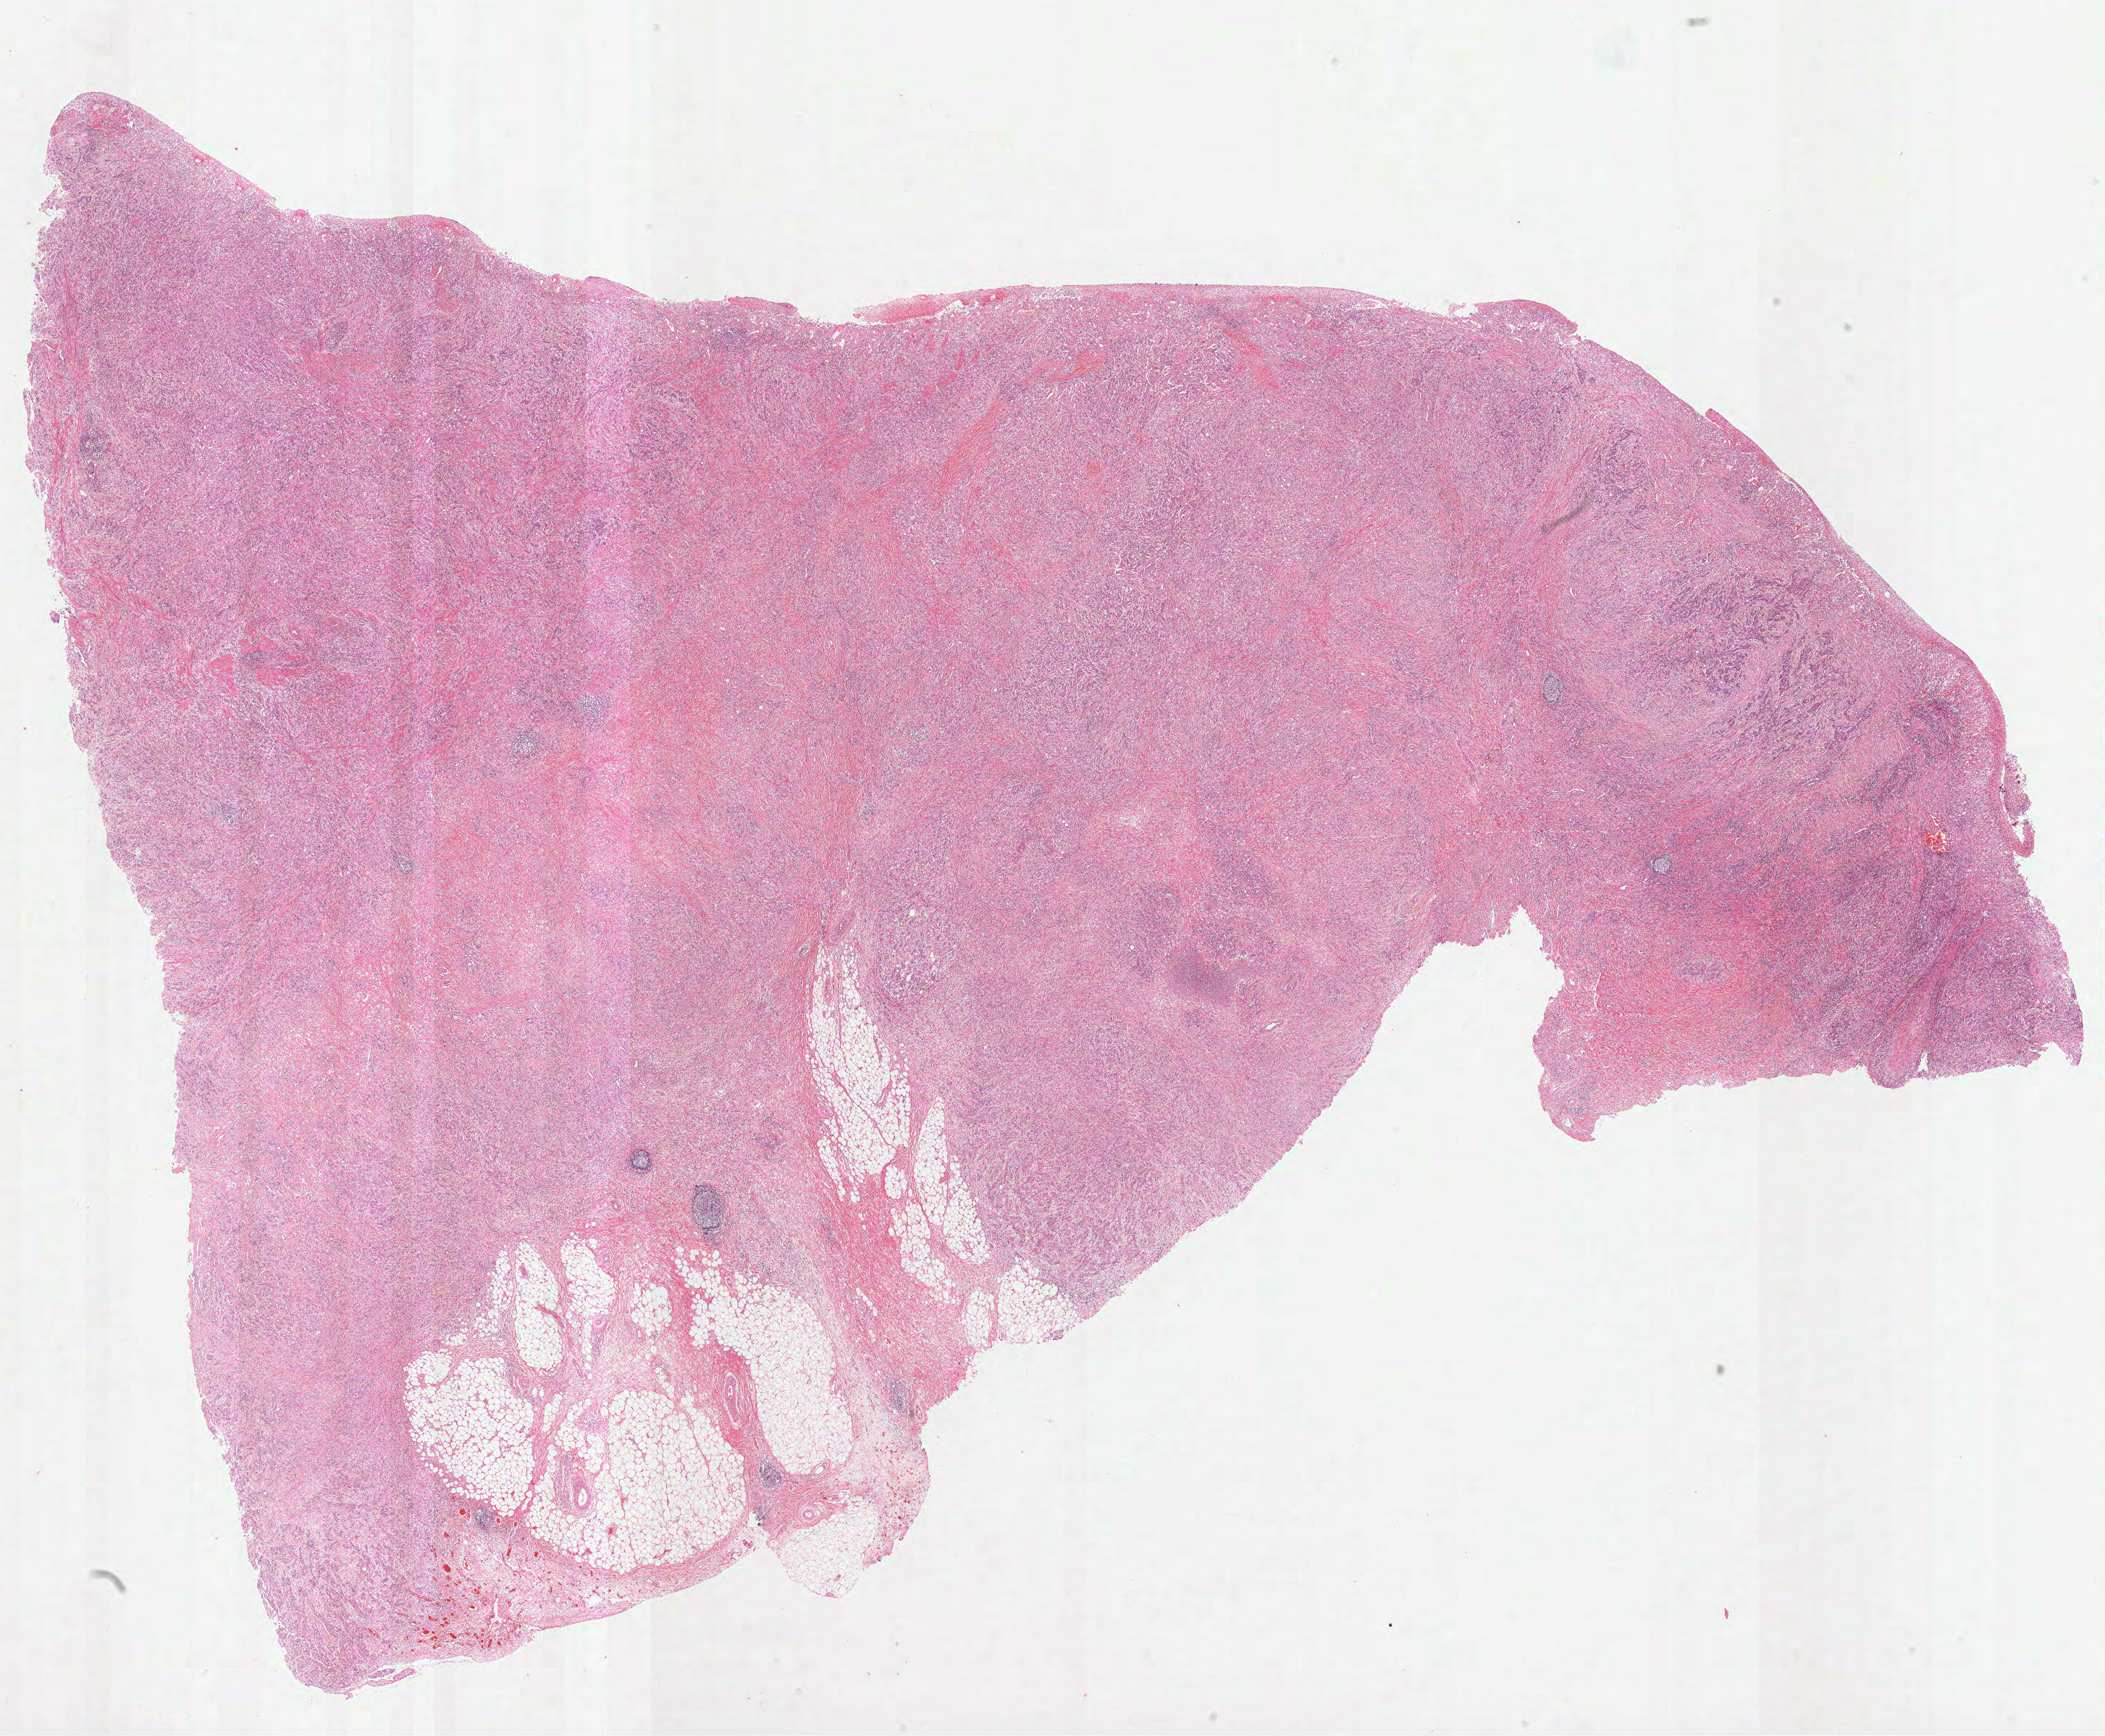
Digitized H&E tissue section (whole slide), whole scanned area (about 23.4 x 19.3 mm) shown as a low-resolution overview. FFPE section. Stomach, primary tumour sample. Female patient; age at initial diagnosis 80 years. Histologic grade: G3 (poorly differentiated).
Lymph nodes positive (case pathology): 0 of 15 examined. AJCC pathologic stage: IIA (7th edition). Diagnosis: Adenocarcinoma, NOS (fundus of stomach).